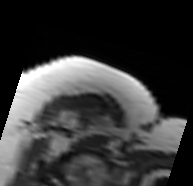
MRI of an extremity soft-tissue mass, one axial slice. Slice 65 of 91 in the series (ordered by position). MR volume resampled by the dataset authors to the PET/CT grid (not the native acquisition matrix). 3.27 mm slice thickness. 193 × 186 image matrix, field of view 188 × 182 mm. Female patient. Case-level facts recorded for this patient, not image findings: histological type: malignant solitary fibrous tumor; grade: intermediate; site of the primary tumour: right thigh.
Annotated regions visible in this slice (expert contour drawn on MRI and transferred to this co-registered scan by the dataset authors):
- gross tumour volume including surrounding oedema: bounding box [x1, y1, x2, y2] px = [49, 108, 114, 150]